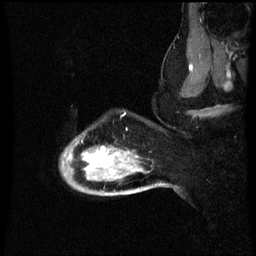
Breast MRI (dynamic contrast-enhanced), one sagittal slice; position 52 of 60 along the scan axis; dynamic contrast-enhanced series, image 2 of 3 at this slice position (ordered by acquisition); 1.5 T; TE 4.2 ms, TR 8.9 ms; 2 mm slice thickness; 256 × 256 image matrix, field of view 200 × 200 mm. Patient: female, 49 years. From the clinical record (not read from this slice): setting: breast cancer imaged before/during neoadjuvant chemotherapy; receptor status: HR-positive, HER2-negative.
Structures marked on this image (semi-automatically segmented with operator editing):
- analysis volume of interest (the breast-tissue region the enhancement analysis was run in; not a lesion): bounding box <62,132,159,197> (left, top, right, bottom; pixels)
- tumour enhancement mask (voxels above the 70 % enhancement threshold inside the analysis volume of interest): <84,148,125,171>